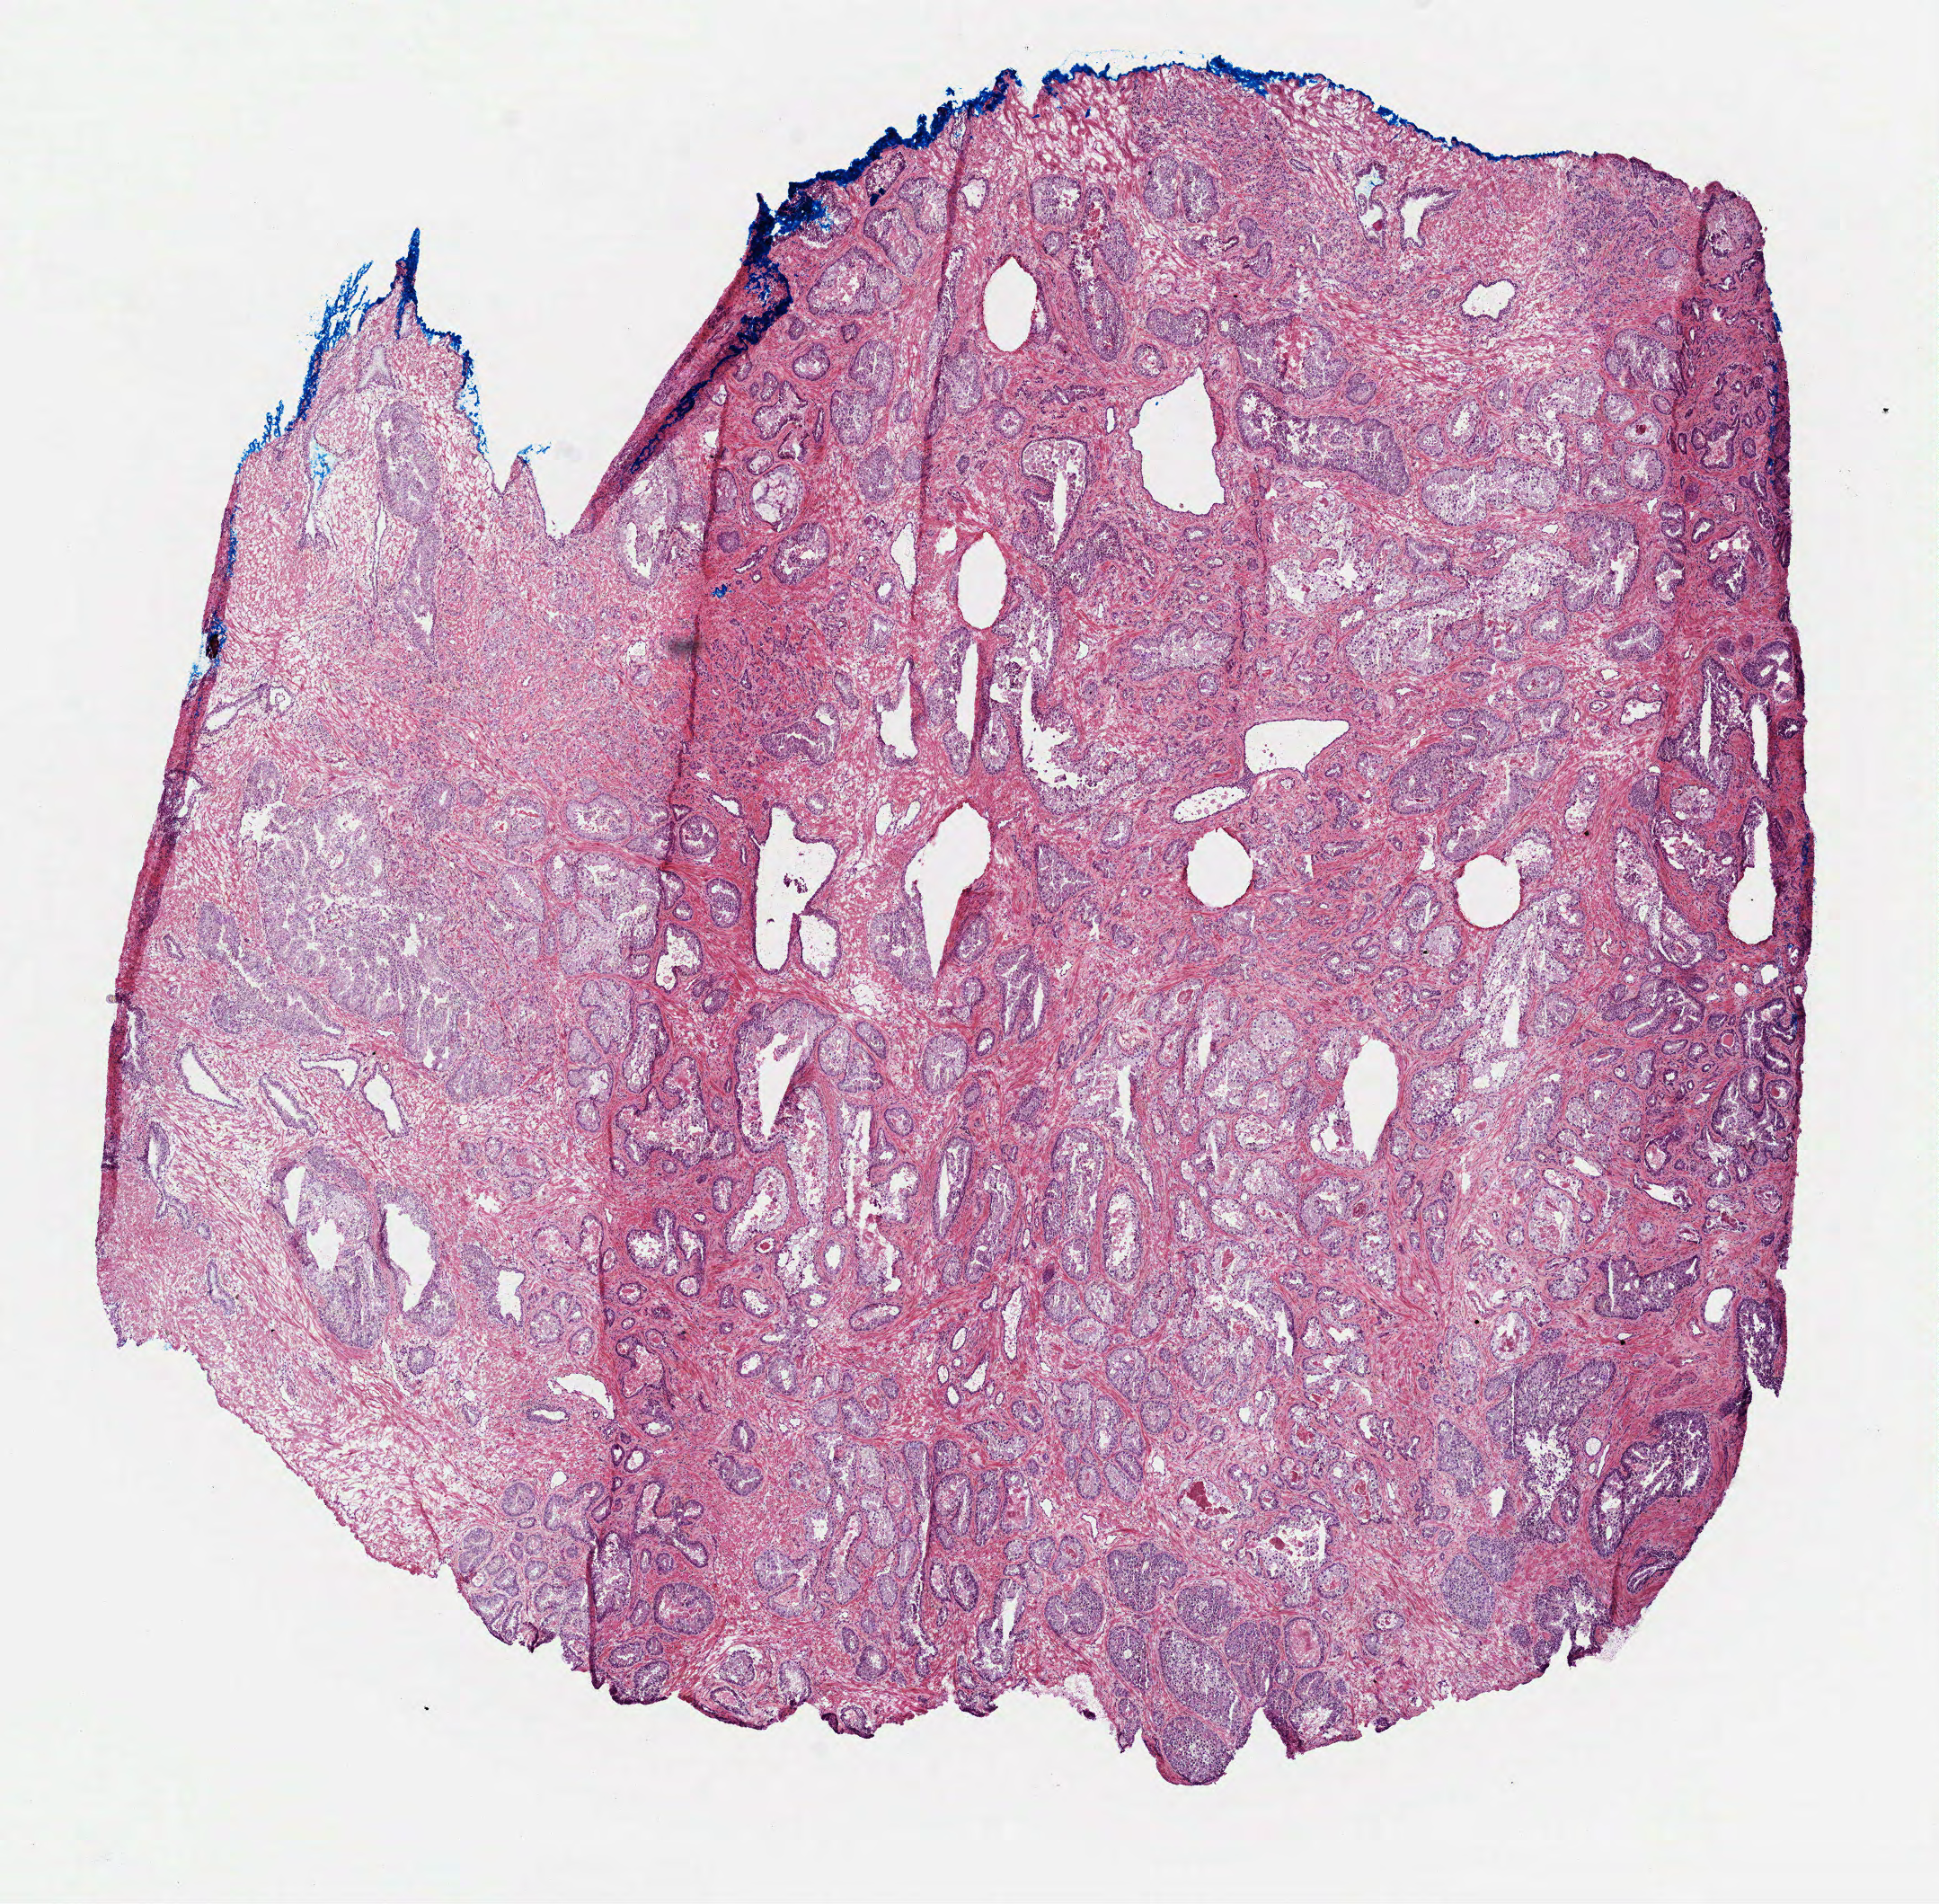
H&E-stained whole-slide image — a low-resolution overview of the entire scanned area, about 8.7 x 8.5 mm, frozen section from the top of the tissue portion, prostate, primary tumour sample. Male, age 66 years at initial diagnosis. Gleason score: 9 (4+5). Slide review estimates, as recorded: tumour nuclei 65%, necrosis 0%.
• diagnosis: Acinar cell carcinoma (prostate gland)
• laterality: bilateral